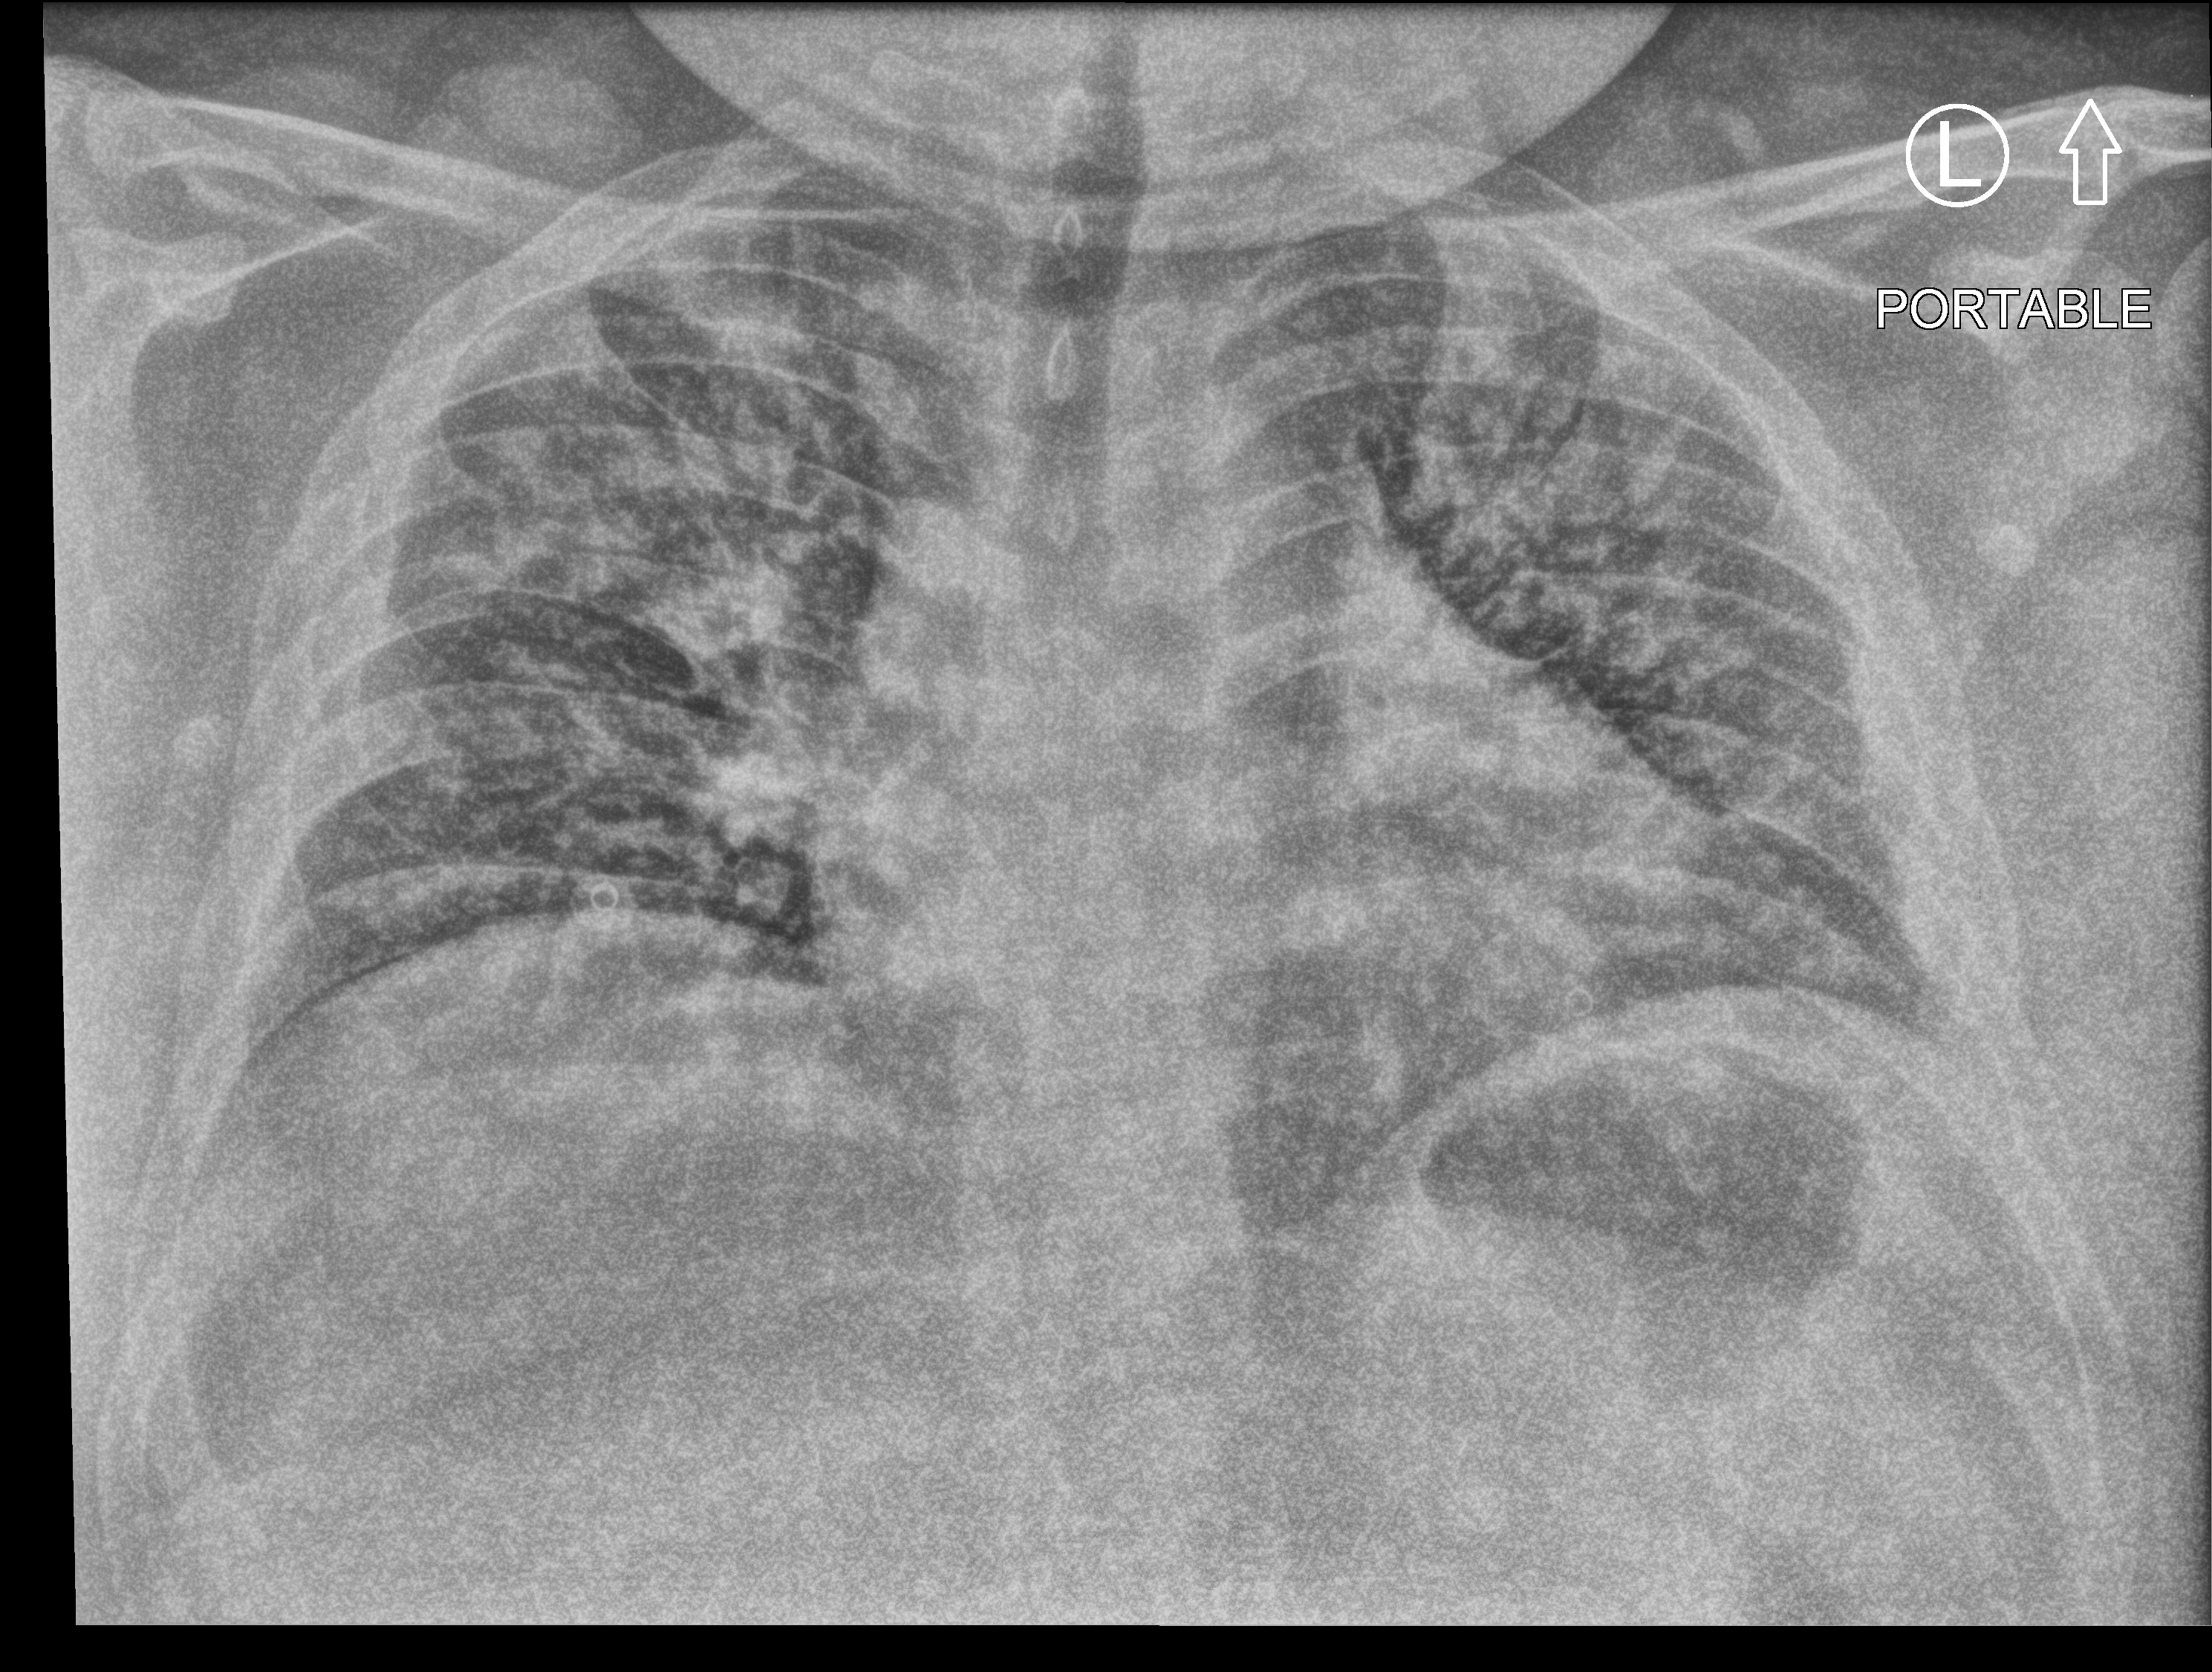
Chest X-ray (portable). Male patient hospitalised with COVID-19, age 18–59 years.
Admission-level facts for this patient (not findings on this image; timing relative to this image not recorded): admitted to intensive care during this hospital stay: no; length of hospital stay: 12 days.